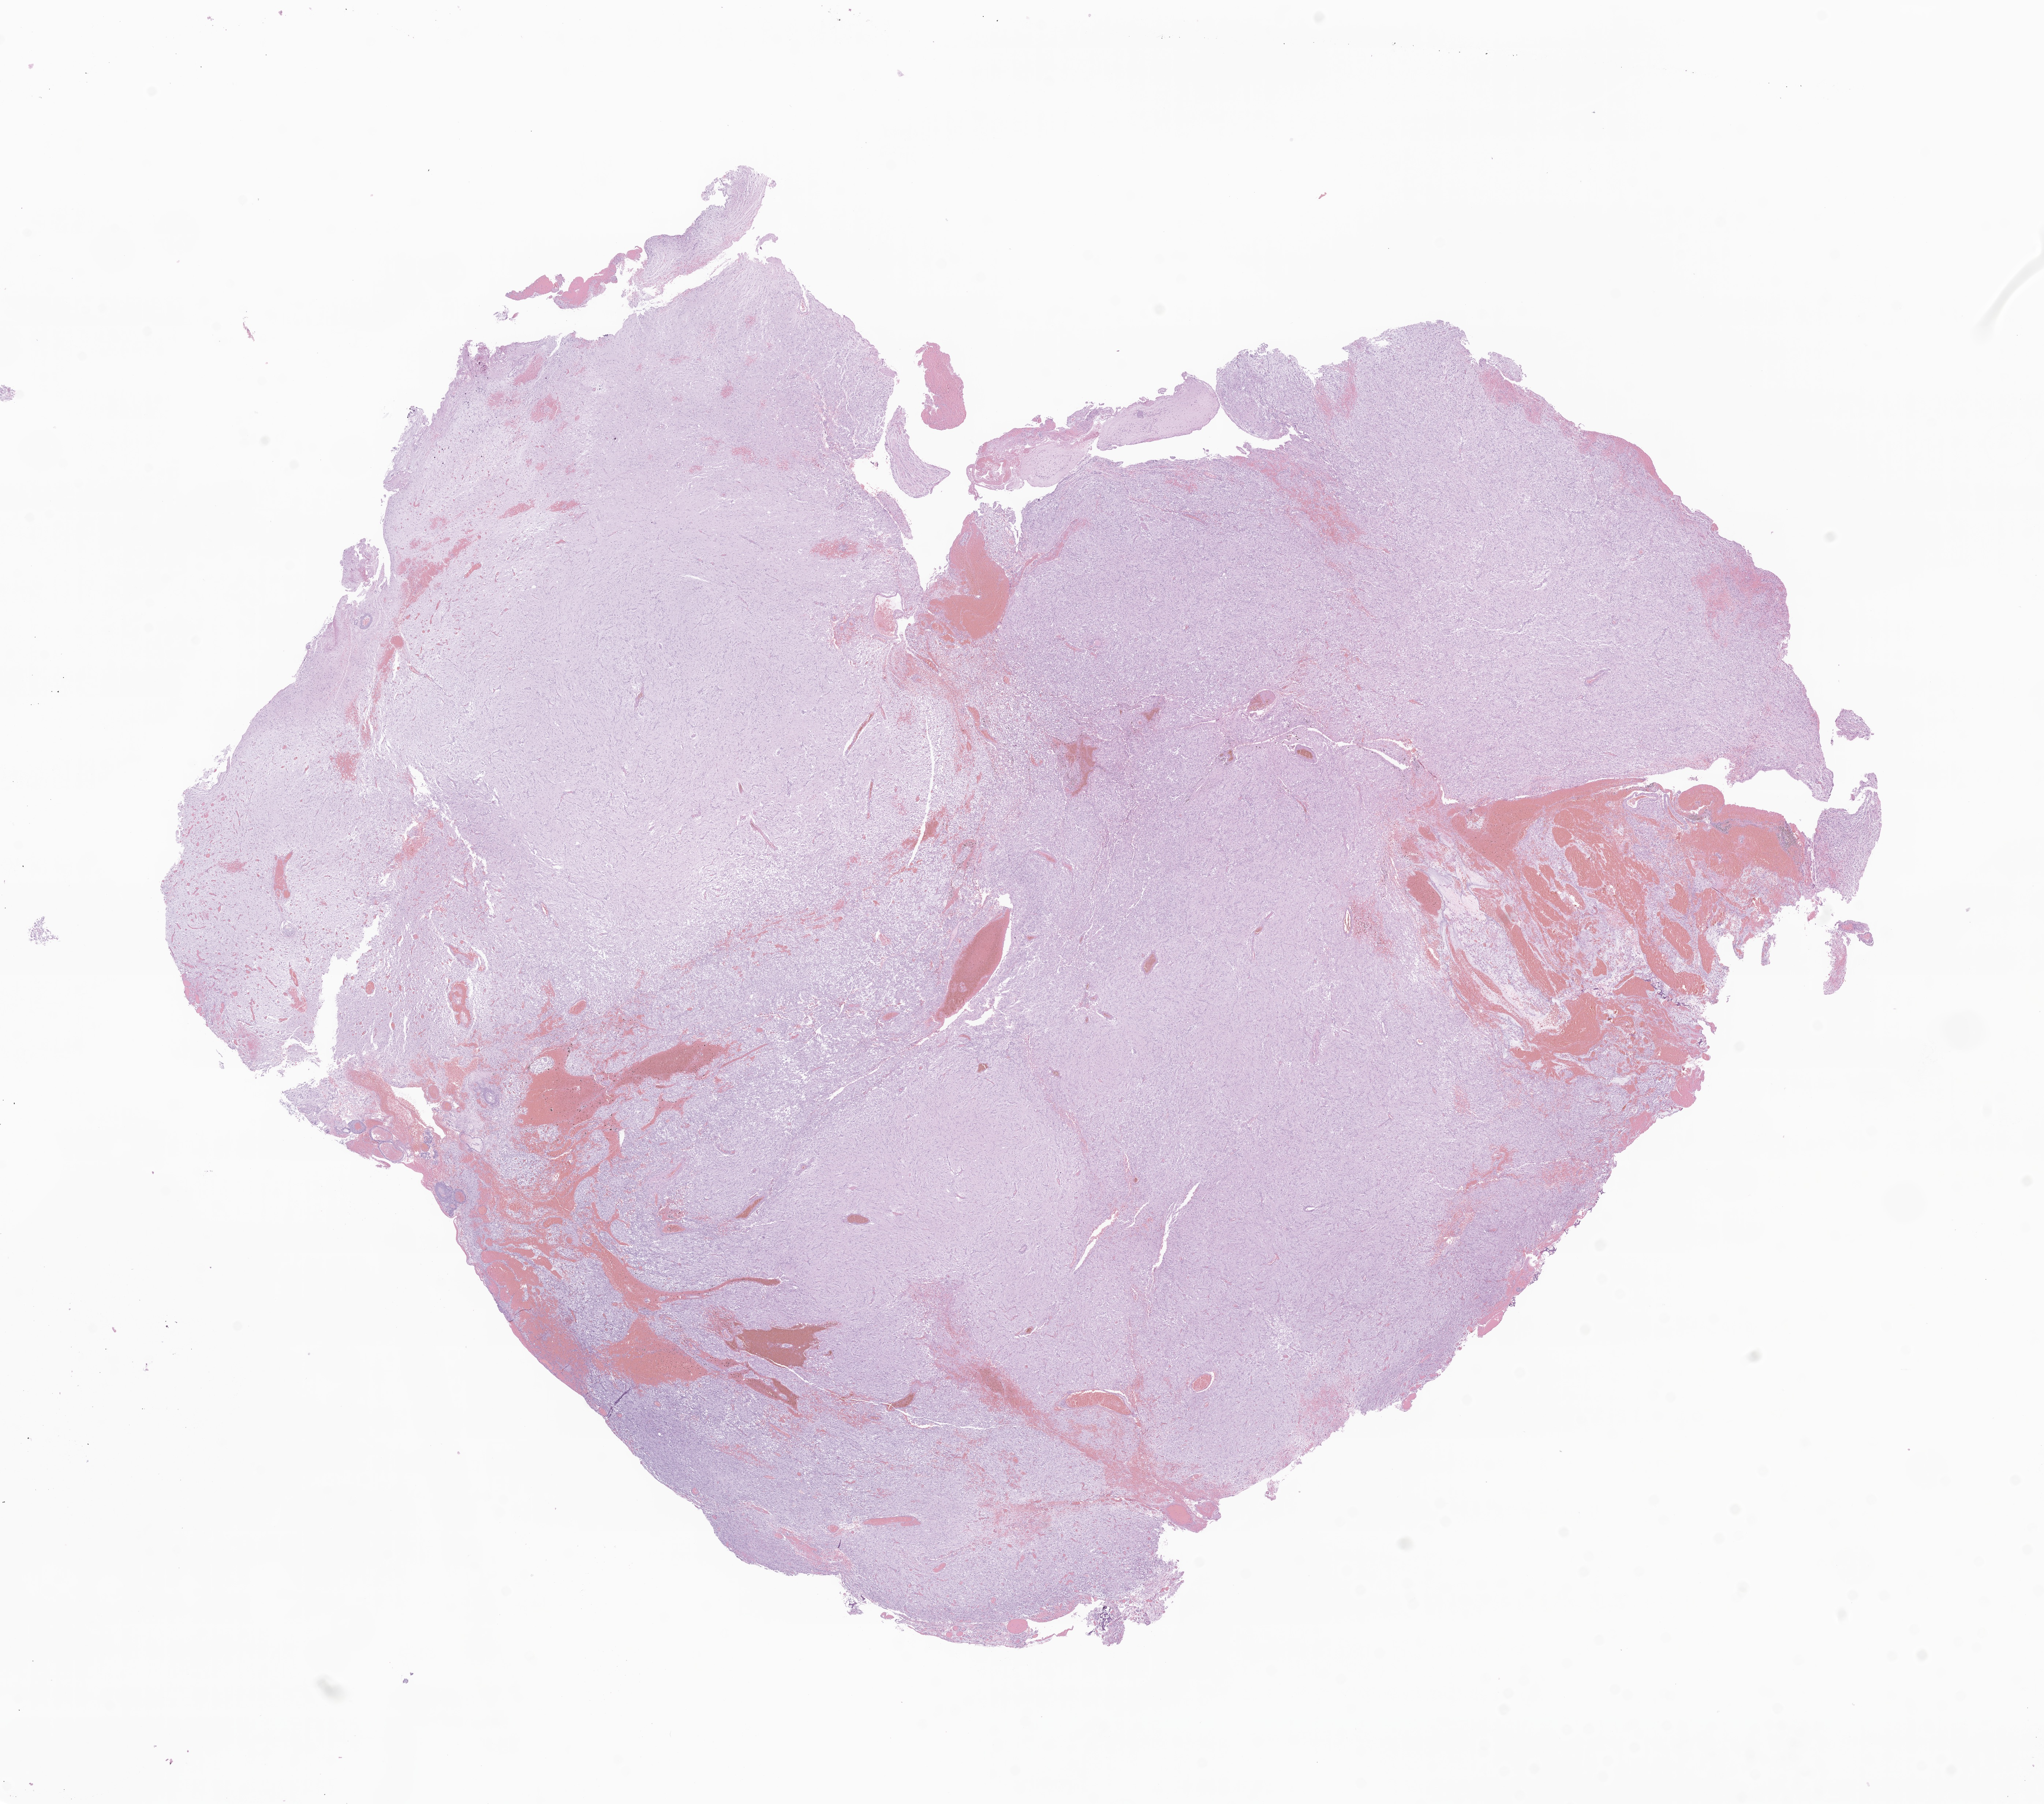
Whole-slide image, haematoxylin and eosin stain of tumor tissue from the brain stem — shown as a low-resolution overview of the whole scanned area (about 23.5 x 20.8 mm), formalin-fixed paraffin-embedded section. Female patient, age 34 months (2 years 10 months).
- diagnosis: Pilocytic astrocytoma